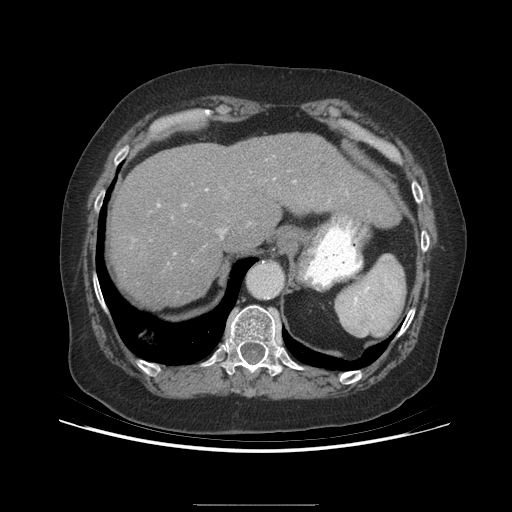
Contrast-enhanced abdominal CT (liver protocol), one axial slice. Slice 171 of 192 in the series (ordered by position). Reconstruction kernel STANDARD. 140 kVp. Soft-tissue window (W 400 / L 40 HU). 2.5 mm slice thickness. 512 × 512 image matrix, field of view 400 × 400 mm. Case-level facts recorded for this patient, not image findings: diagnosis: hepatocellular carcinoma (patient treated with transarterial chemoembolisation; whether this scan precedes or follows treatment is not stated here); TNM stage (as recorded): Stage-I; Child-Pugh class: A; tumour nodularity: uninodular.
Annotated regions visible in this slice (semi-automatically segmented with operator editing):
- liver parenchyma outside the tumour (the mass and vessels are separate outlines, so this box may not span the whole liver): bounding box (x1, y1, x2, y2) in pixels: (110, 132, 398, 306)
- liver vessels: (158, 189, 208, 206)